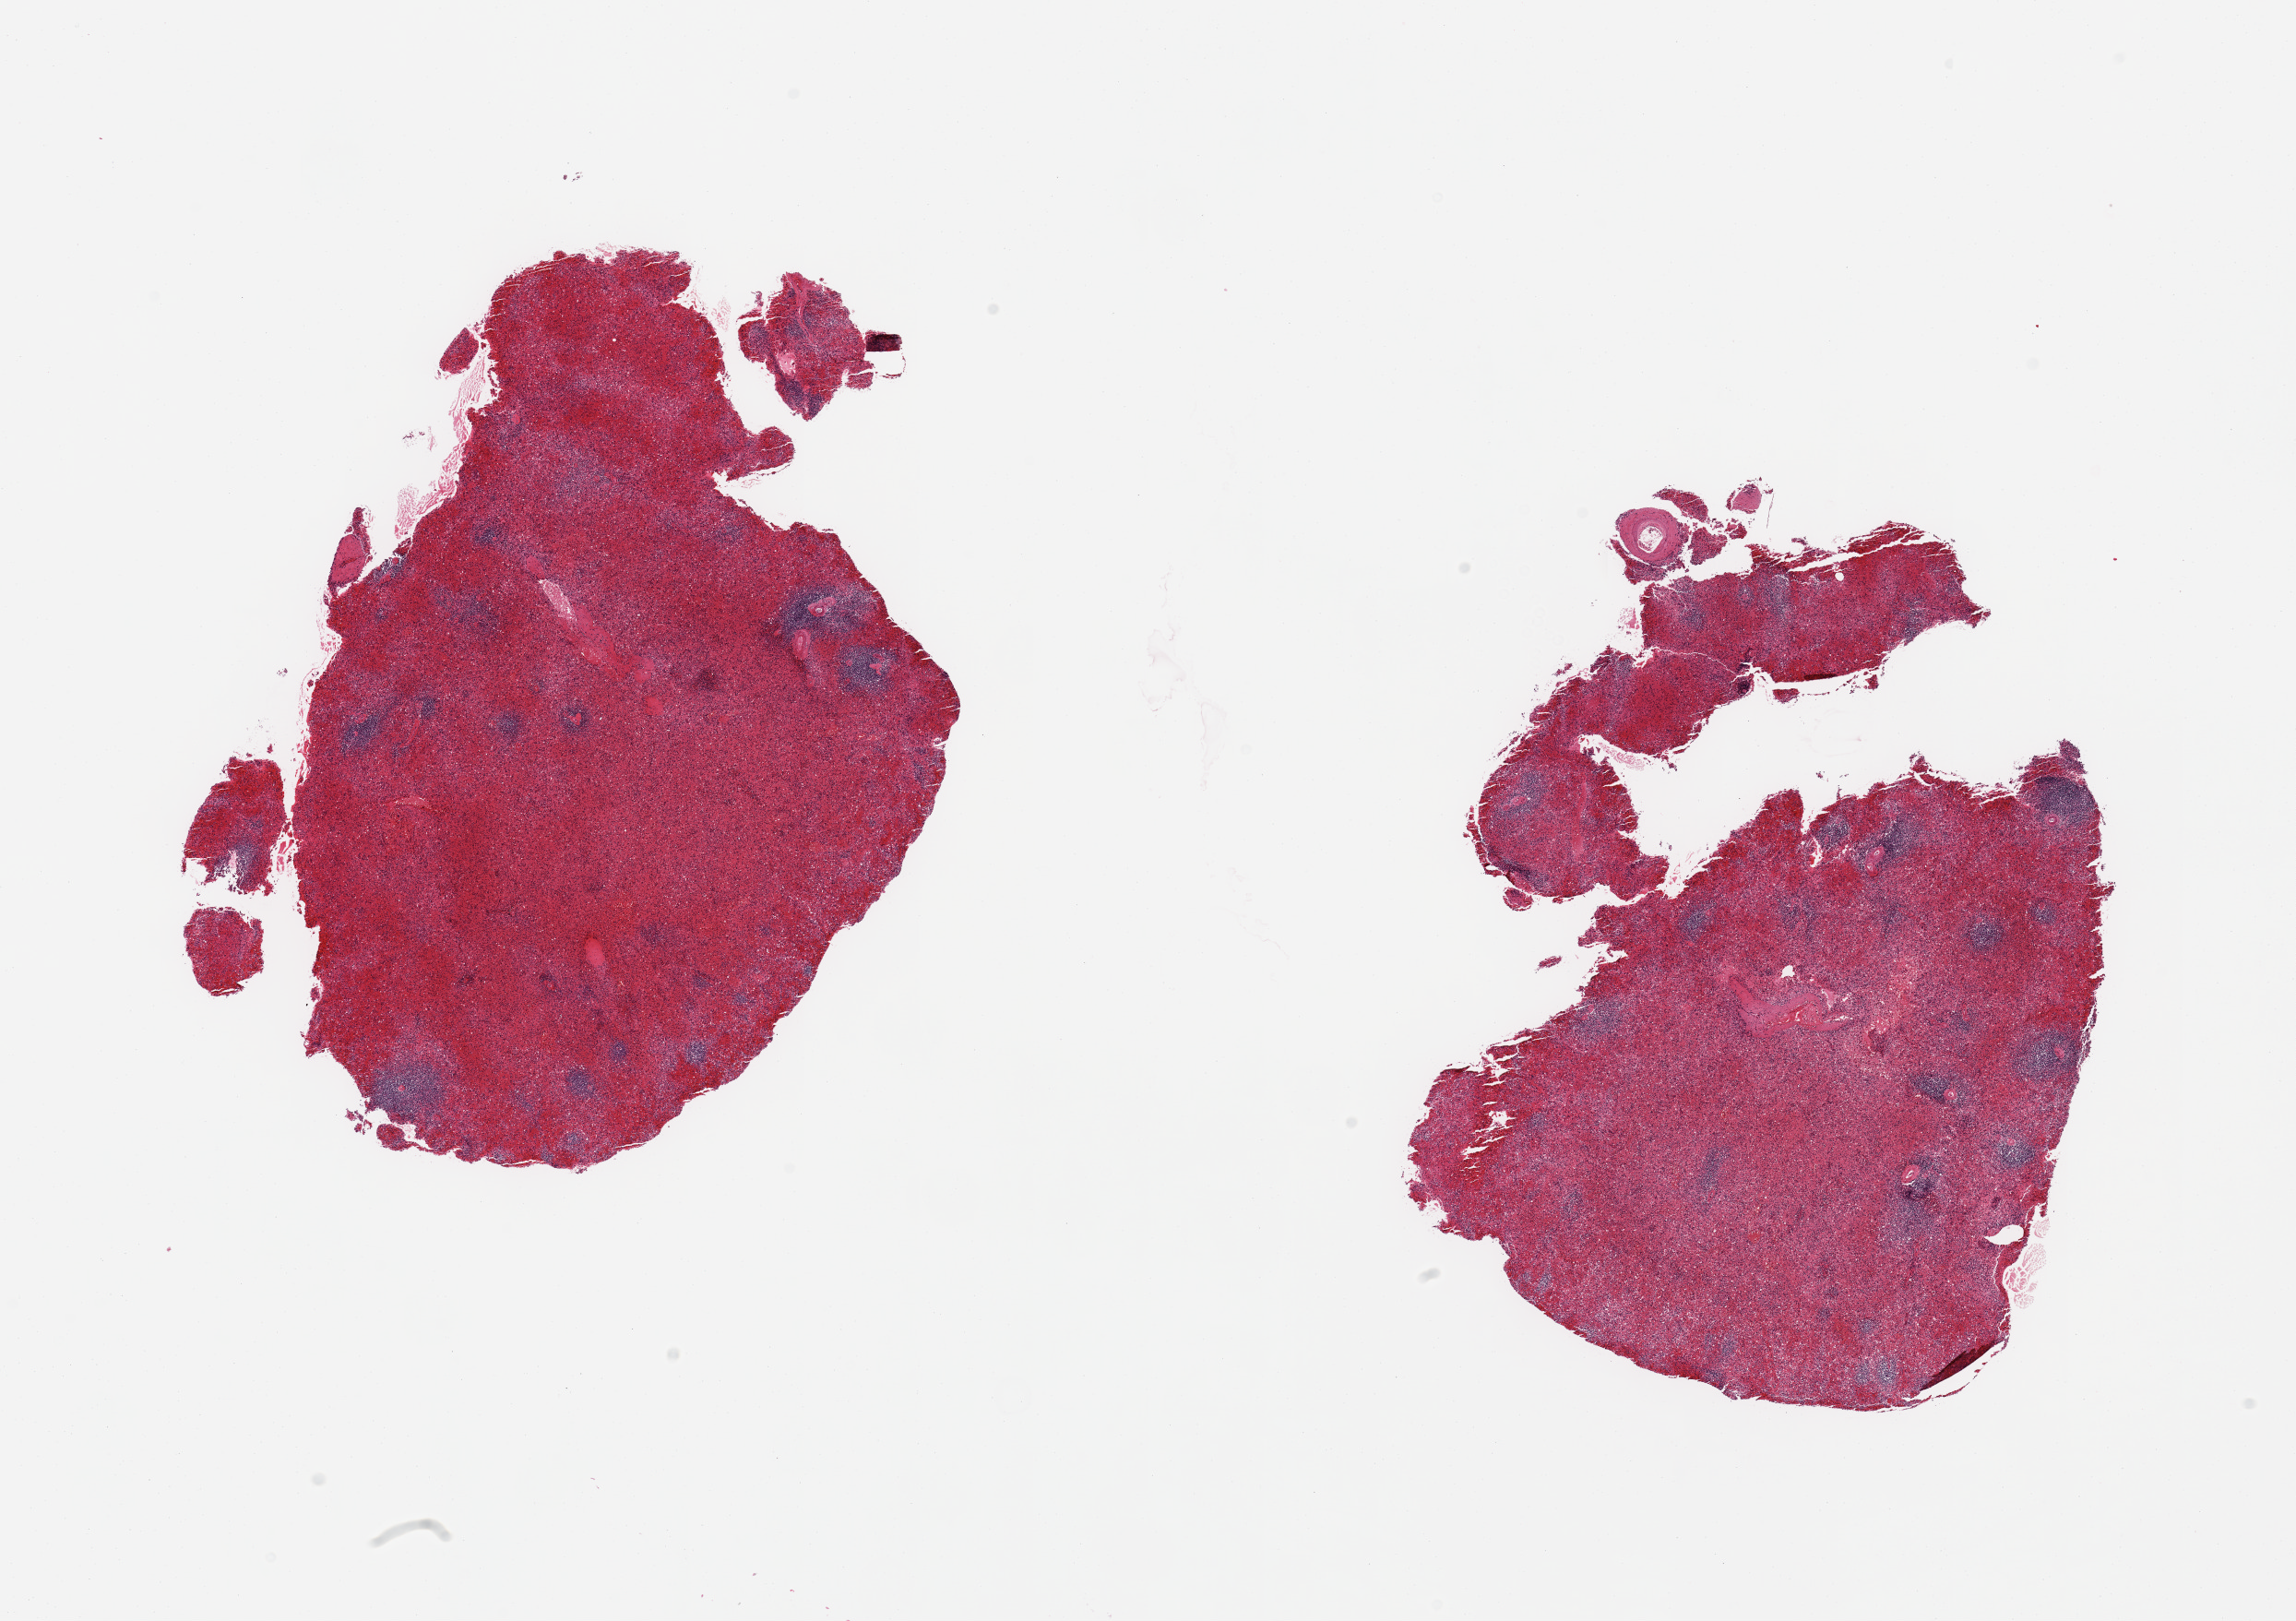
Whole-slide image, H&E stain, brightfield, a low-resolution overview of the entire scanned area, about 19.7 x 13.9 mm; PAXgene-fixed, paraffin-embedded tissue; section of spleen (target tissue); donor tissue sample. Female donor.
* review note (as recorded): 2 pieces; marked congestion